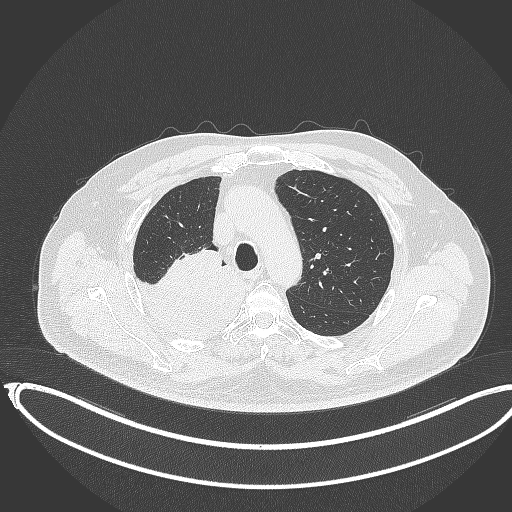
Chest CT, one axial slice. Position 269 of 403 along the scan axis. Lung window (W 1500 / L -600 HU). 1 mm slice thickness. 512 × 512 image matrix, field of view 436 × 436 mm. Male patient, age 68 years. Case-level facts recorded for this patient, not image findings: clinical TNM (as recorded): T2a N0 M0.
Annotated regions visible in this slice (bounding box drawn by a radiologist):
- lung tumour (recorded histology: adenocarcinoma): bounding box <134,248,251,337> (left, top, right, bottom; pixels)